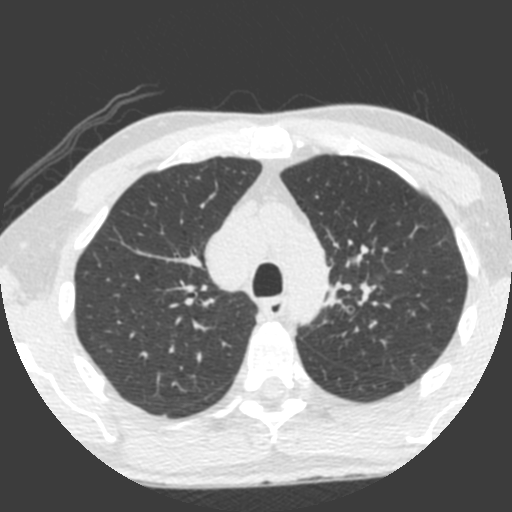
Low-dose screening chest CT, axial slice, third screening round (two years after baseline), lung window (W 1500 / L -600 HU), 2 mm slice thickness, slice 158 of 212 in the series. Male participant, aged 55 years at enrolment. Current smoker at enrolment.
• Lesion marked by an expert reader, box from (x=308, y=237) to (x=387, y=322) px.
• The exam's reader record, not a measurement of the box and not confirmed to be the same lesion: non-calcified nodule or mass ≥4 mm, left upper lobe, 49 × 29 mm, spiculated (stellate) margins, soft tissue attenuation, pre-existing on the prior screen: yes; interval growth: yes.
• Lung cancer was diagnosed 0 days after this screen: small cell carcinoma, NOS, left upper lobe, undifferentiated (G4), stage IV (AJCC 6th edition), 60 mm at pathology.